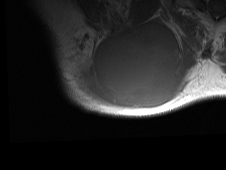
MRI of an extremity soft-tissue mass, one axial slice. Position 52 of 81 along the scan axis. MR volume resampled by the dataset authors to the PET/CT grid (not the native acquisition matrix). 3.27 mm slice thickness. 226 × 170 image matrix. Male patient. From the clinical record (not read from this slice): histological type: pleiomorphic spindle cell undifferentiated; grade: high; site of the primary tumour: right parascapusular.
Structures marked on this image (expert contour drawn on MRI and transferred to this co-registered scan by the dataset authors):
- gross tumour volume including surrounding oedema: box from (x=65, y=19) to (x=196, y=112) px
- gross tumour volume (mass): (x=92, y=26)–(x=180, y=107)